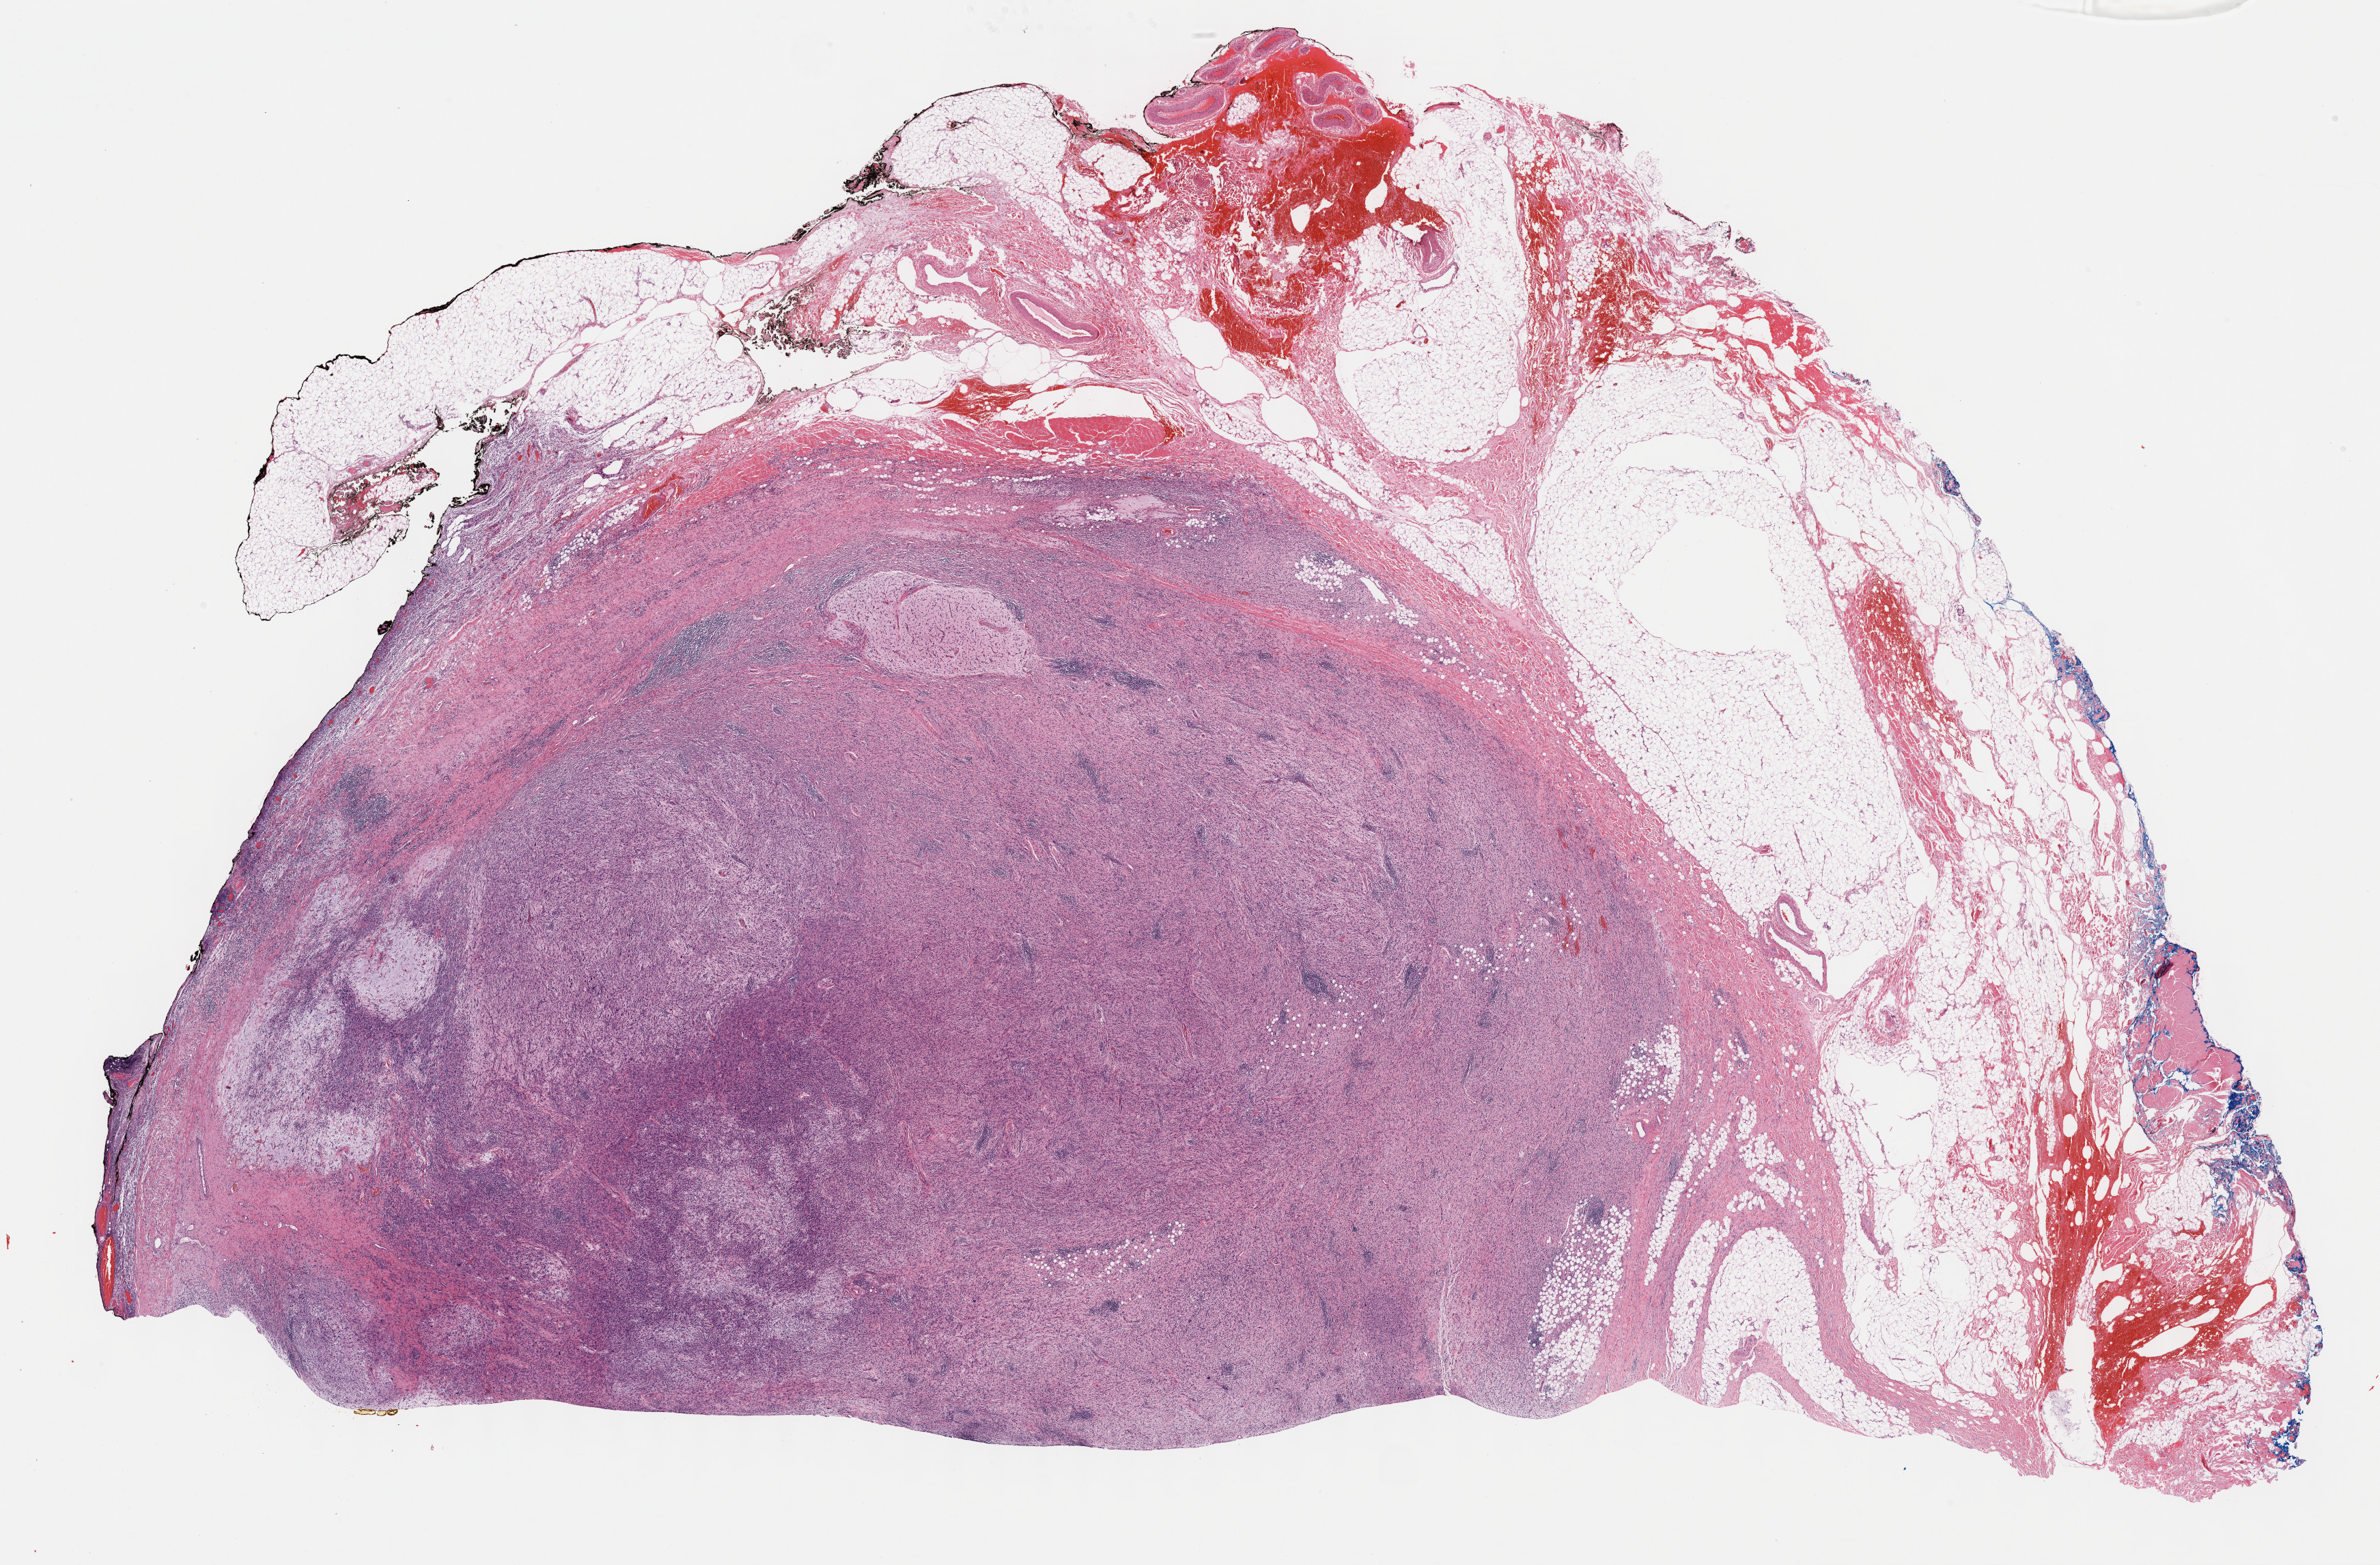
Digitized H&E-stained tissue section (whole slide), low-resolution overview of the scanned area, about 28.2 x 18.5 mm (acquisition: 40x scan); formalin-fixed paraffin-embedded (FFPE) diagnostic section; connective, subcutaneous and other soft tissues, primary tumour sample. Patient: male, age at initial diagnosis 35 years.
- diagnosis: Fibromyxosarcoma